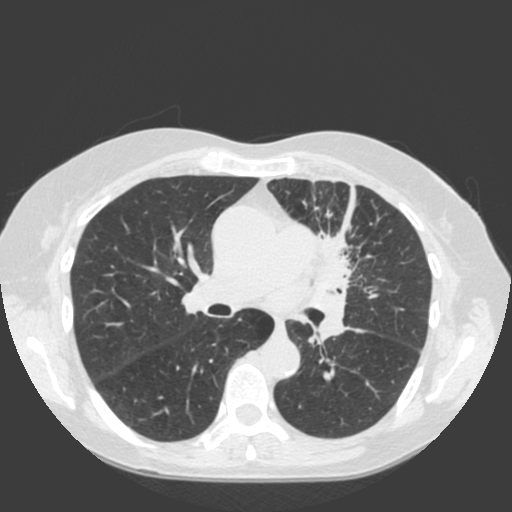
Axial slice from a low-dose chest CT screening exam, baseline screening round, lung window (W 1500 / L -600 HU), 512 × 512 image matrix, field of view 350 × 350 mm. Female participant, aged 66 years at enrolment. Current smoker at enrolment.
• Expert-annotated lung lesion, bounding box <277,203,402,316> (left, top, right, bottom; pixels).
• The exam's reader record, not a measurement of the box and not confirmed to be the same lesion: non-calcified nodule or mass ≥4 mm, left upper lobe, 61 × 45 mm, spiculated (stellate) margins, soft tissue attenuation.
• Later outcome: lung cancer diagnosed 19 days after this screen — squamous cell carcinoma, keratinizing, NOS, left upper lobe, left hilum, mediastinum, left main stem bronchus, other location, poorly differentiated (G3), stage IIIB (AJCC 6th edition), 60 mm at pathology.